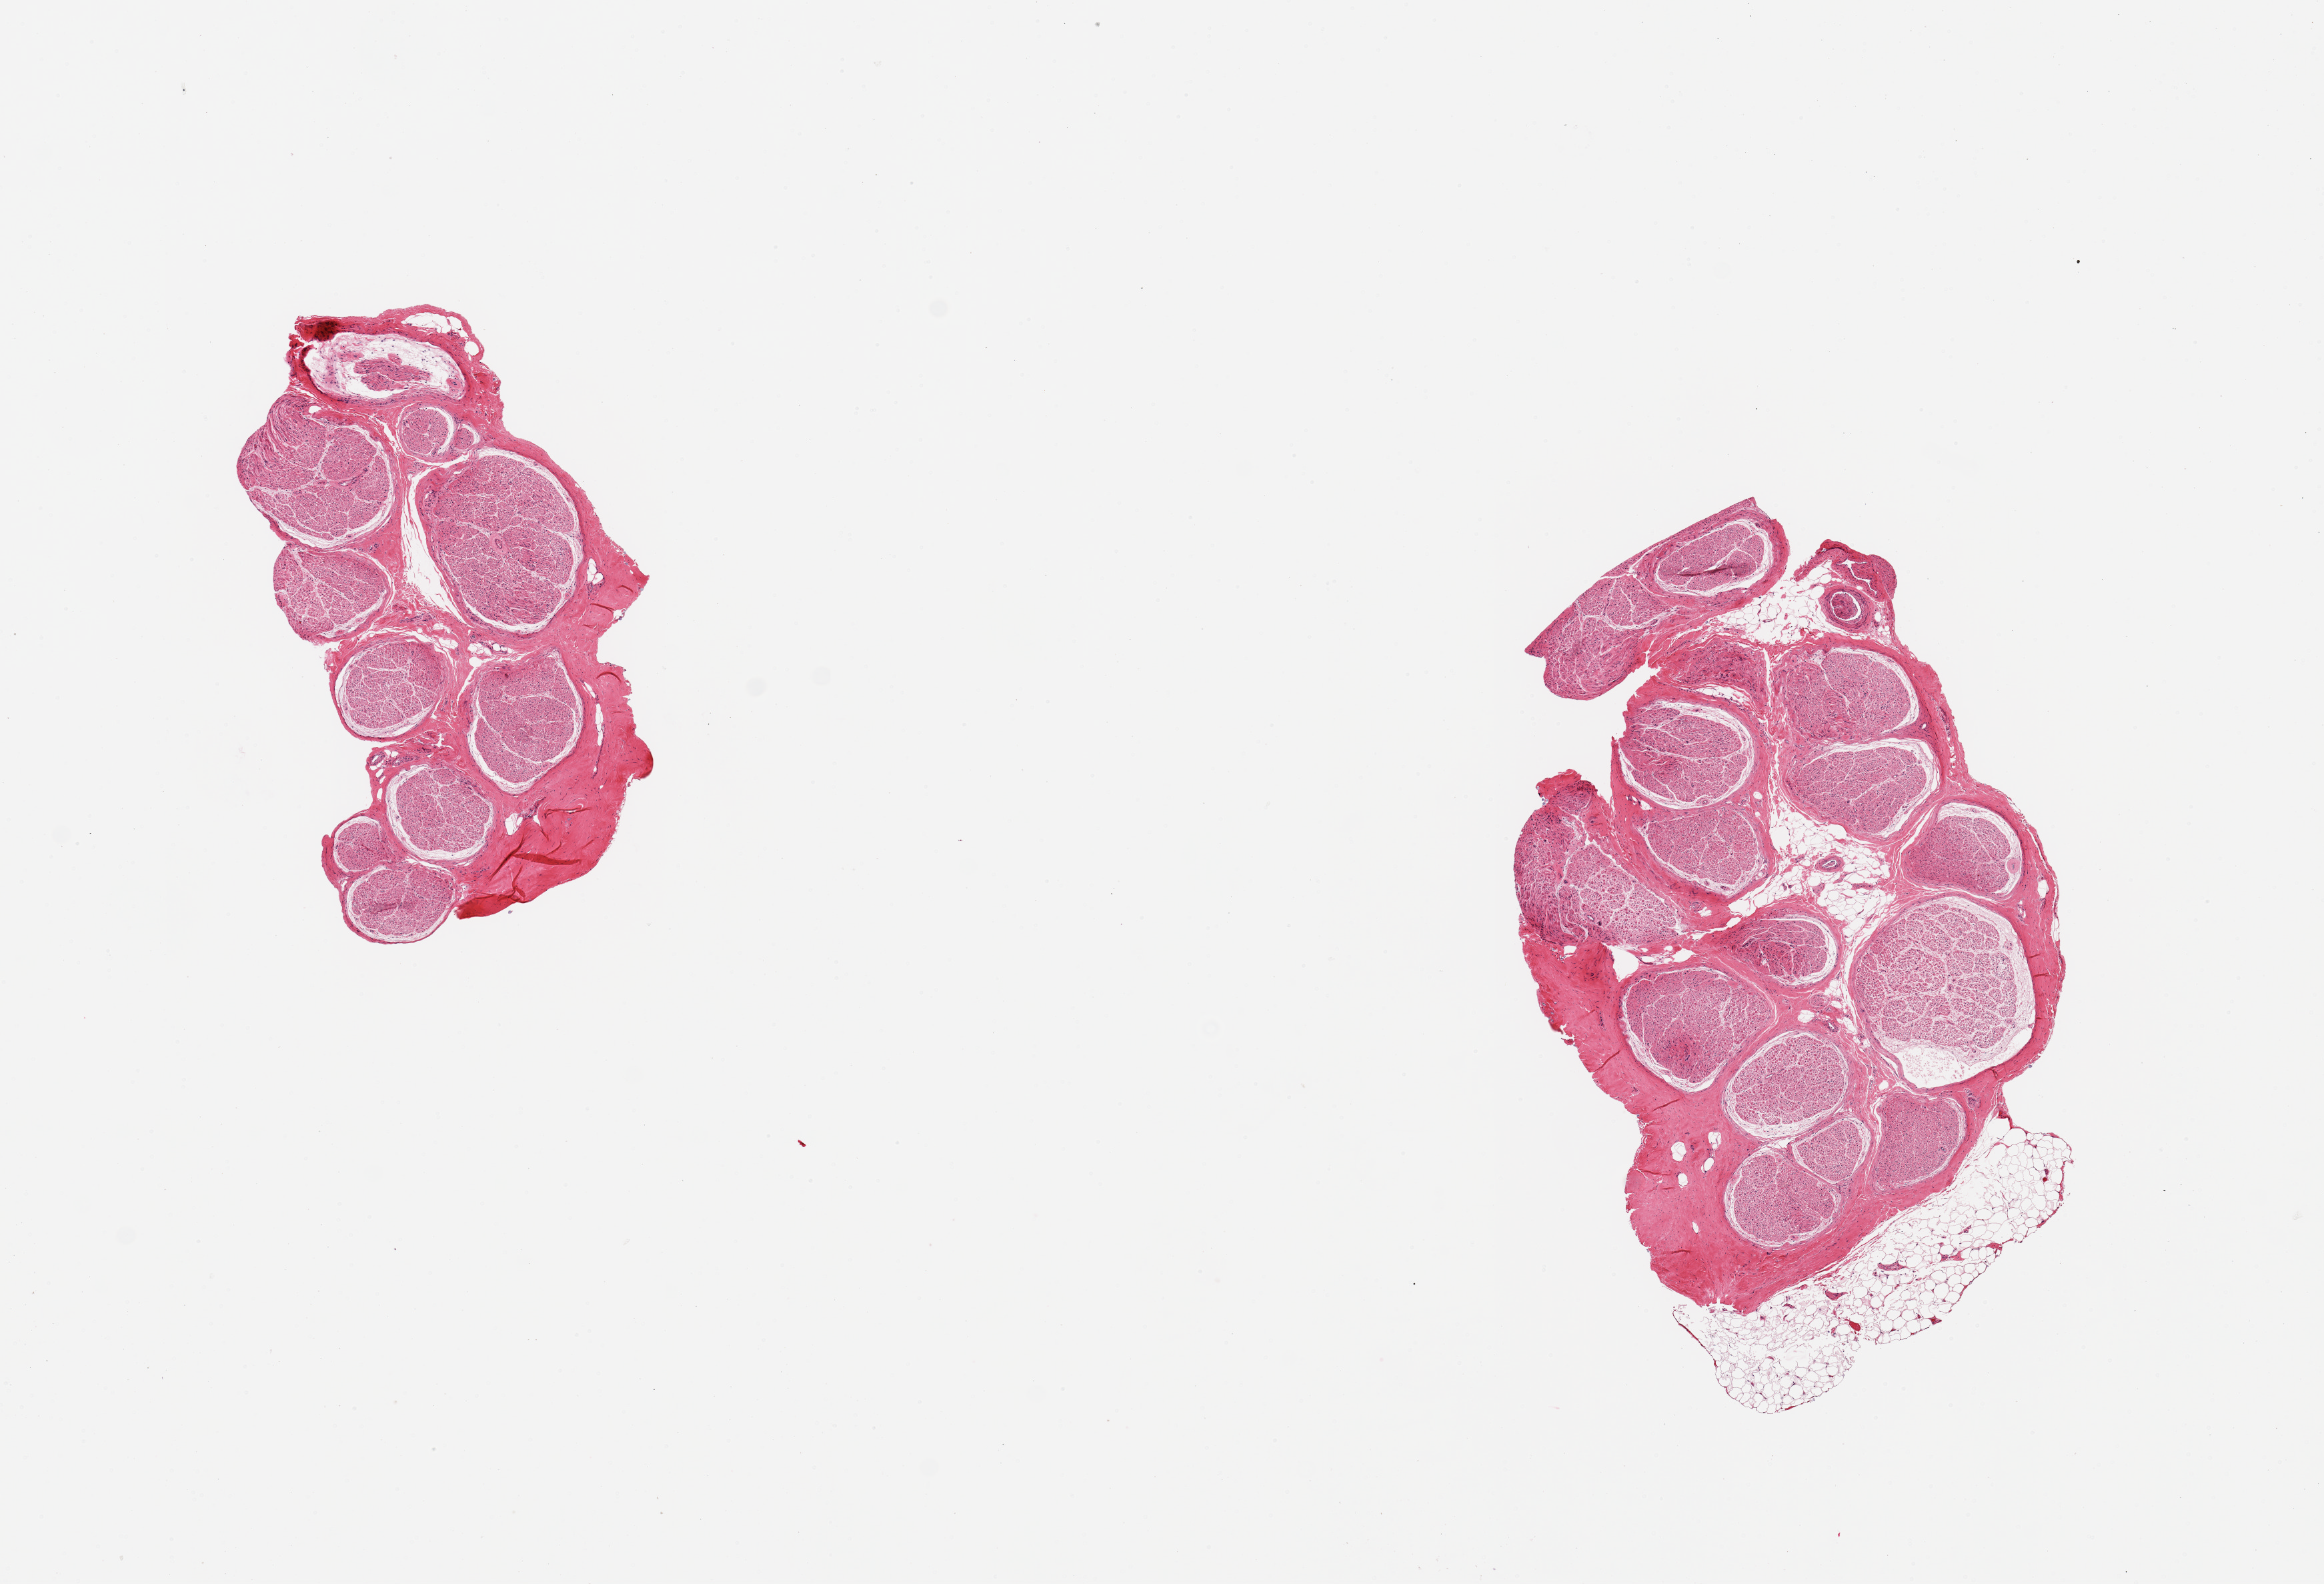
Digitized hematoxylin and eosin (H&E)-stained section — a low-resolution overview of the entire scanned area, about 13.8 x 9.4 mm (acquisition: 20x scan), PAXgene-fixed paraffin-embedded (PFPE) section, section of tibial nerve (target tissue), donor tissue sample. Donor sex: male.
Review note (as recorded): 2 pieces; one with 10-20% external (predominant) and internal fat.